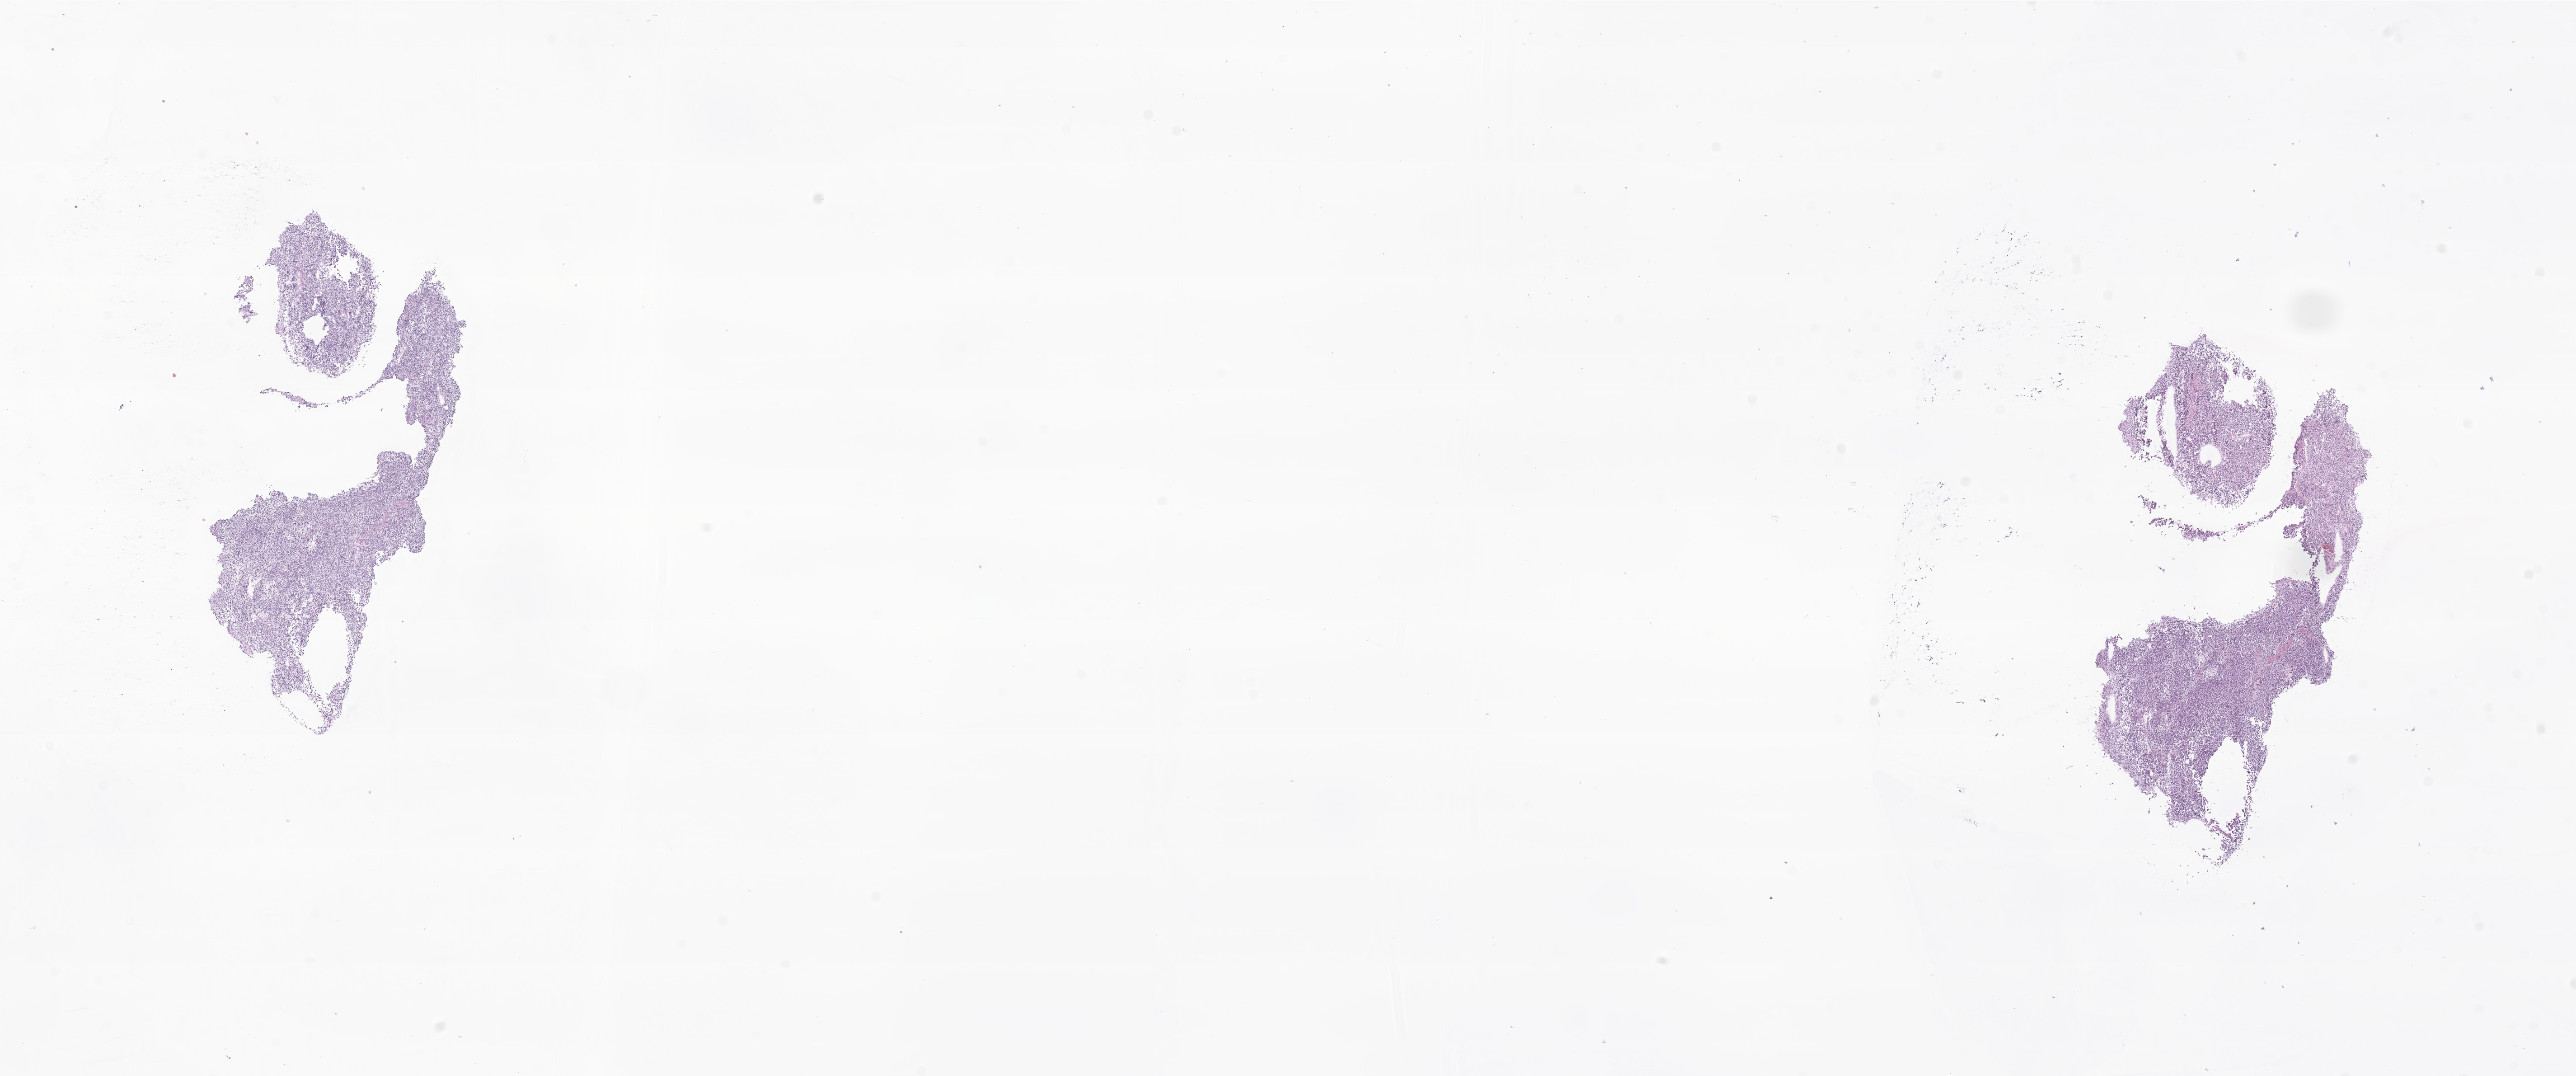
Whole-slide image, hematoxylin and eosin (H&E) stain of tumor tissue from the brain — low-resolution overview of the scanned area, about 24.0 x 10.0 mm, frozen section. Male patient, age 91 months.
Recorded diagnosis: Neoplasm, uncertain whether benign or malignant.